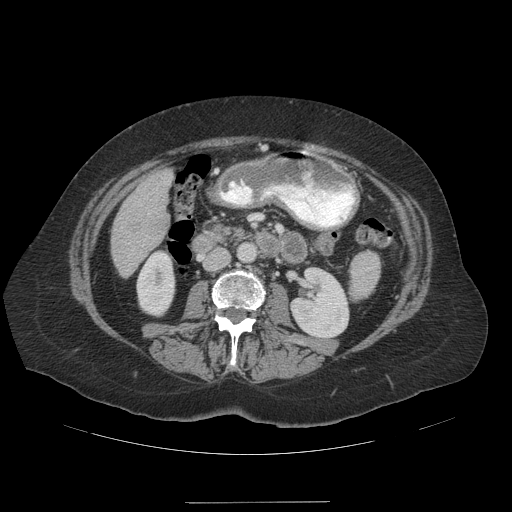
Contrast-enhanced abdominal CT (liver protocol), one axial slice; position 40 of 99 along the scan axis; reconstruction kernel STANDARD; 140 kVp; soft-tissue window (W 400 / L 40 HU); 2.5 mm slice thickness; 512 × 512 image matrix. From the clinical record (not read from this slice): diagnosis: hepatocellular carcinoma (patient treated with transarterial chemoembolisation; whether this scan precedes or follows treatment is not stated here); TNM stage (as recorded): Stage-IVA; Child-Pugh class: A; tumour nodularity: multinodular.
Structures marked on this image (semi-automatically segmented with operator editing):
- liver parenchyma outside the tumour (the mass and vessels are separate outlines, so this box may not span the whole liver): bounding box (x1, y1, x2, y2) in pixels: (112, 170, 172, 276)